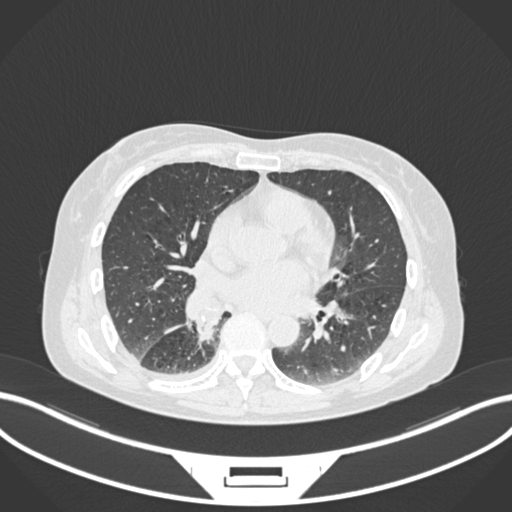
Chest CT, one axial slice. Slice 78 of 168 in the series (ordered by position). Lung window (W 1500 / L -600 HU). 1 mm slice thickness. 512 × 512 image matrix. Female patient, age 63 years. From the clinical record (not read from this slice): clinical TNM (as recorded): T1c N0 M0.
Annotated regions visible in this slice (bounding box drawn by a radiologist):
- lung tumour (recorded histology: adenocarcinoma): box from (x=188, y=296) to (x=226, y=345) px